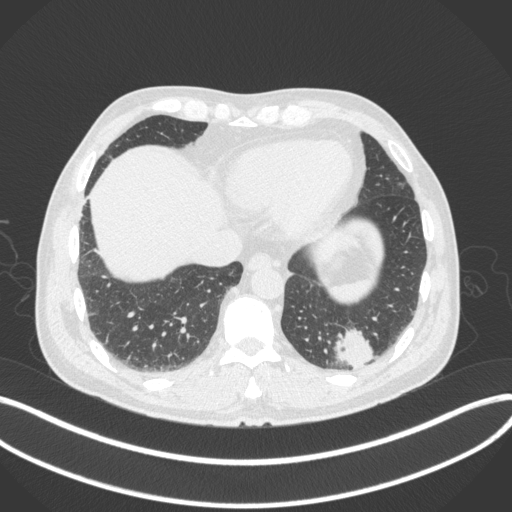
Chest CT, one axial slice; position 65 of 313 along the scan axis; reconstruction kernel B31f; 120 kVp; lung window (W 1500 / L -600 HU); 1 mm slice thickness; 512 × 512 image matrix, field of view 400 × 400 mm. Patient: male, 54 years. From the clinical record (not read from this slice): clinical TNM (as recorded): T1c N0 M1.
Annotated regions visible in this slice (rectangle marked by the reading radiologist):
- lung tumour (recorded histology: adenocarcinoma): bounding box [x1, y1, x2, y2] px = [330, 324, 375, 371]